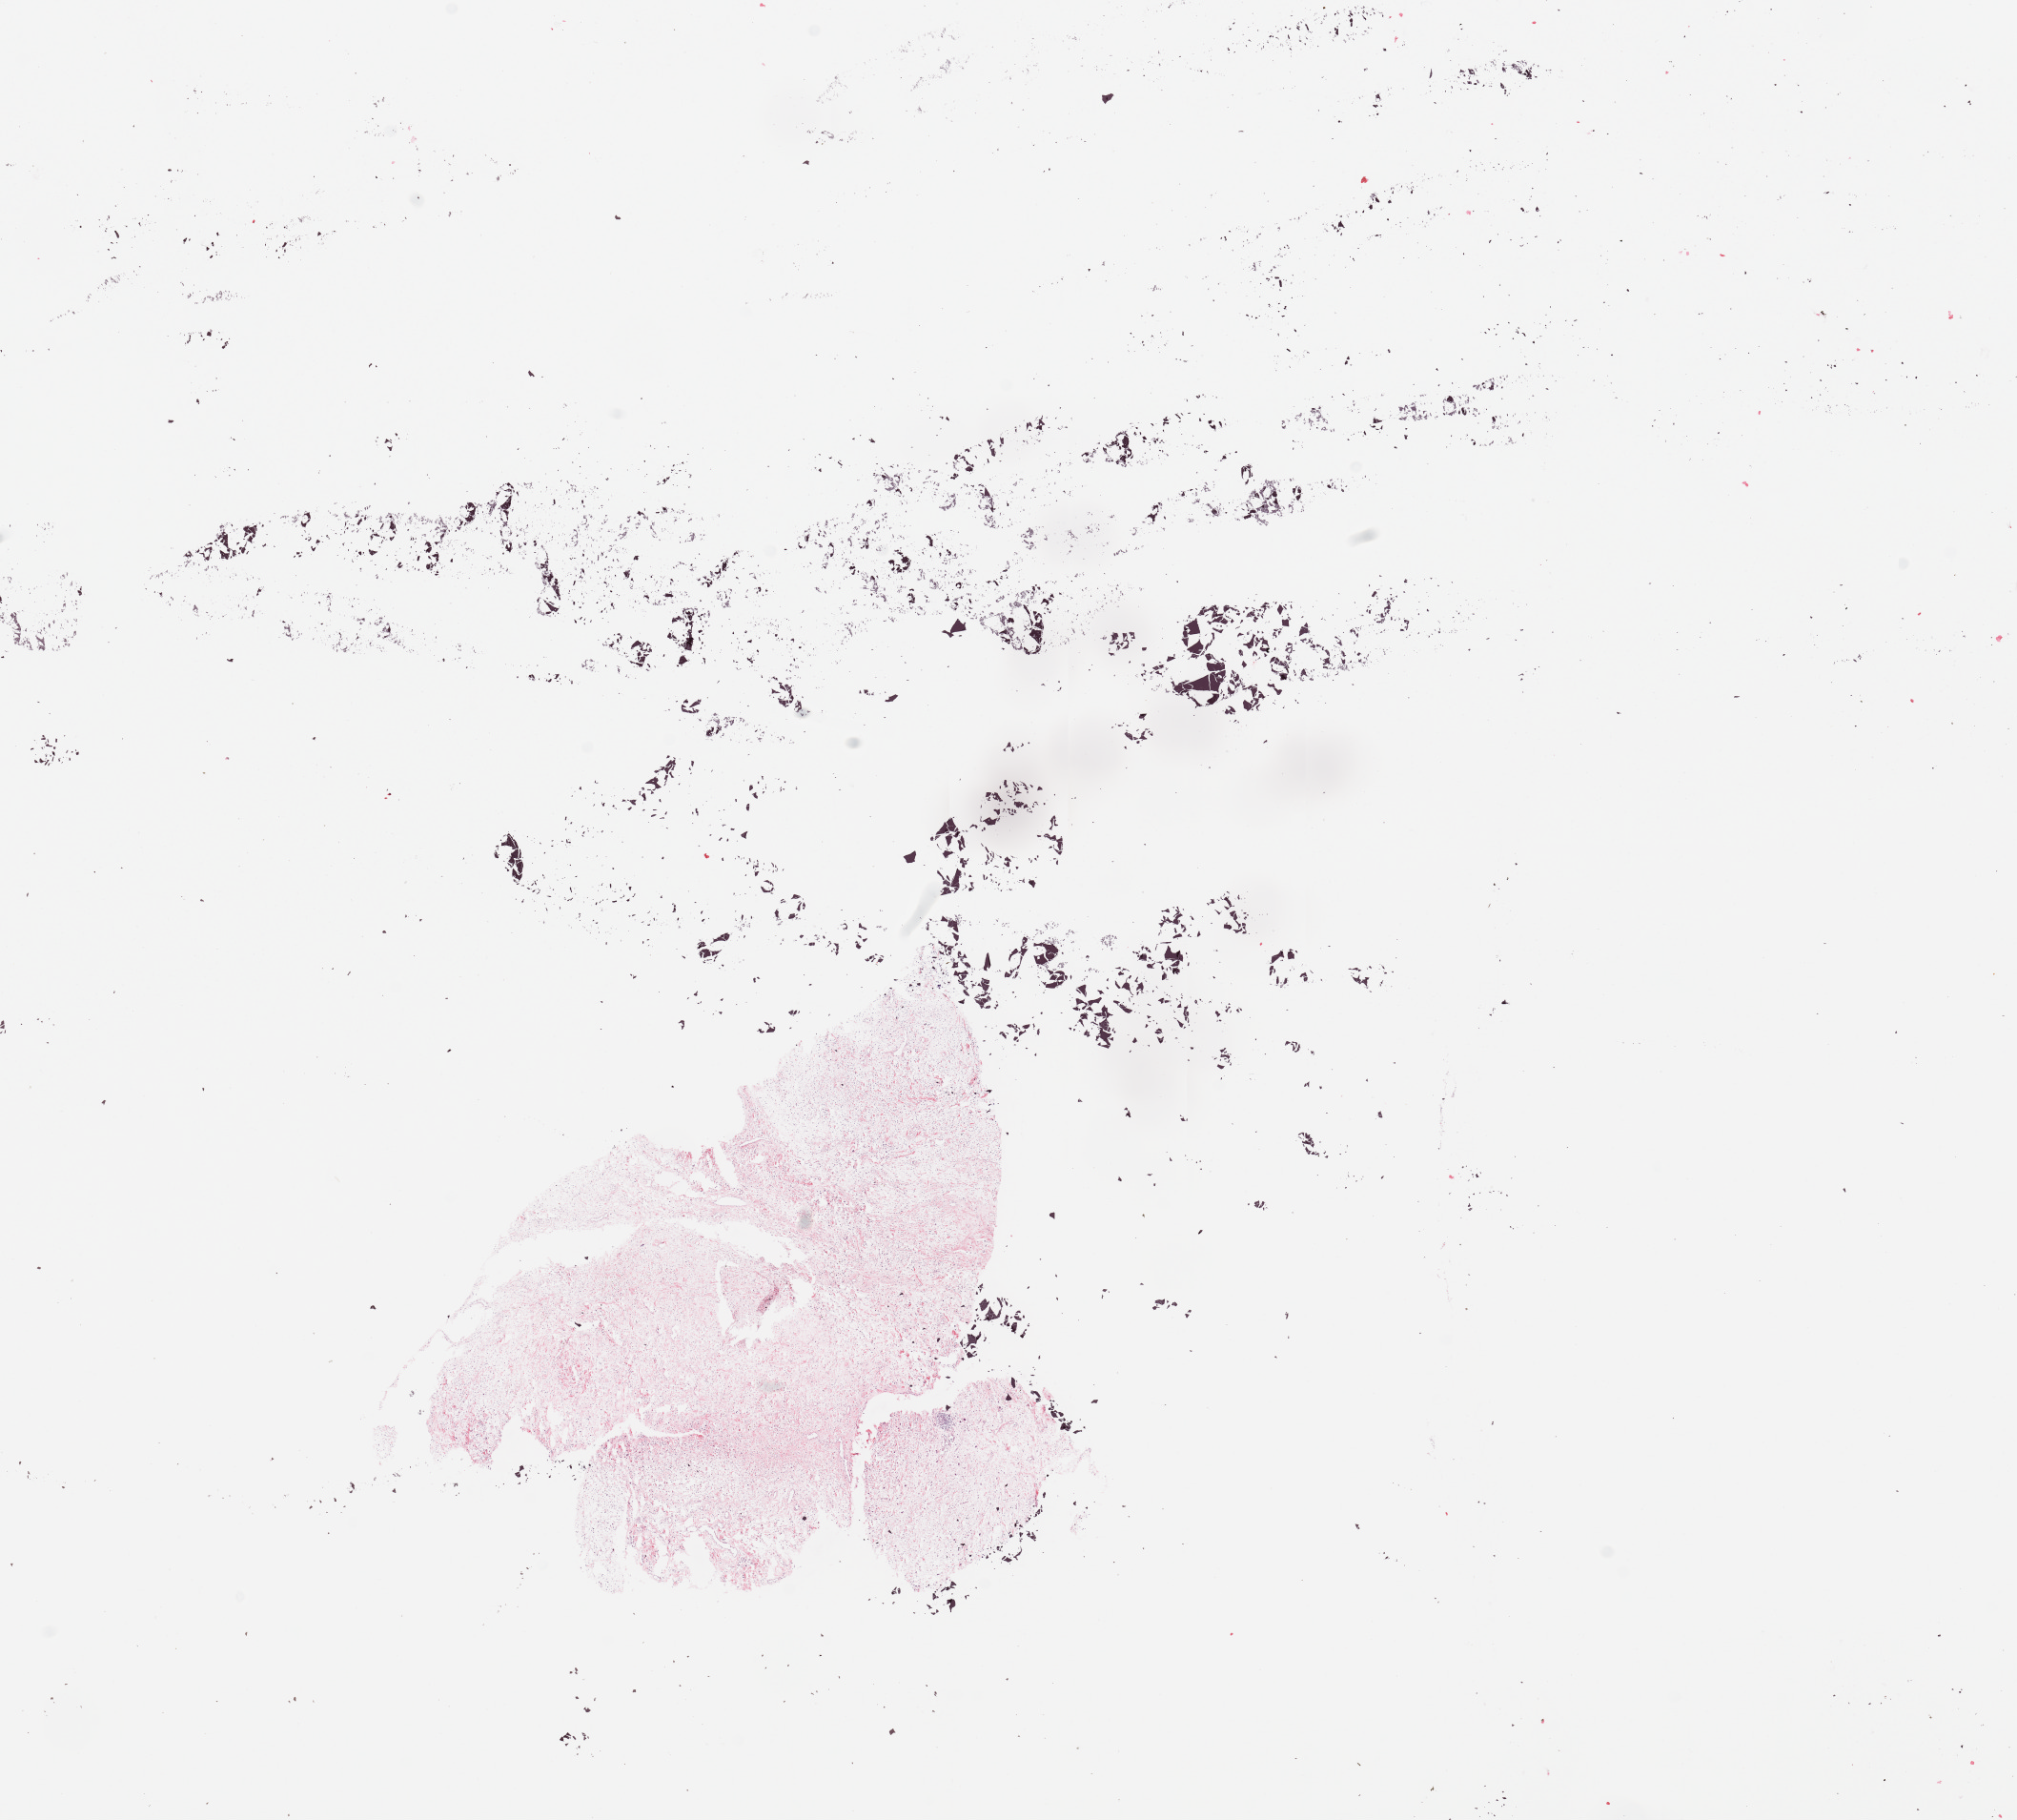
Hematoxylin and eosin (H&E) stained whole-slide image — shown as a low-resolution overview of the whole scanned area (about 16.7 x 15.1 mm, slide scanned at 20x). Tumour tissue sample. 67-year-old male patient.
Primary tumour site (as recorded): lower extremity. Patient diagnosis (cohort enrolment): sarcoma (site not recorded at cohort level).